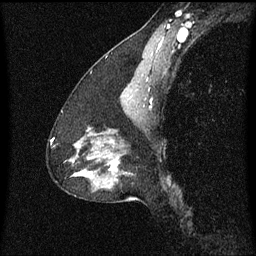
Breast MRI (dynamic contrast-enhanced), one sagittal slice. Position 37 of 60 along the scan axis. Dynamic contrast-enhanced series, image 2 of 3 at this slice position (ordered by acquisition). 1.5 T. TE 4.2 ms, TR 8.4 ms. 2 mm slice thickness. 256 × 256 image matrix, field of view 200 × 200 mm. Patient: female, 47 years.
Annotated regions visible in this slice (semi-automatically segmented with operator editing):
- analysis volume of interest (the breast-tissue region the enhancement analysis was run in; not a lesion): bounding box <81,140,126,191> (left, top, right, bottom; pixels)
- tumour enhancement mask (voxels above the 70 % enhancement threshold inside the analysis volume of interest): <114,166,116,171>